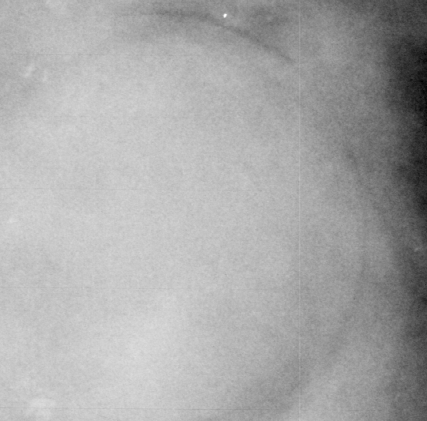
Crop from a digitized film mammogram around one marked abnormality; left breast; CC view; BI-RADS breast density category 4 (scale 1–4).
Mass, shape round, margins circumscribed; BI-RADS assessment category 3; subtlety rating 3 on a 1 (subtle) to 5 (obvious) scale; pathology (as recorded): benign.